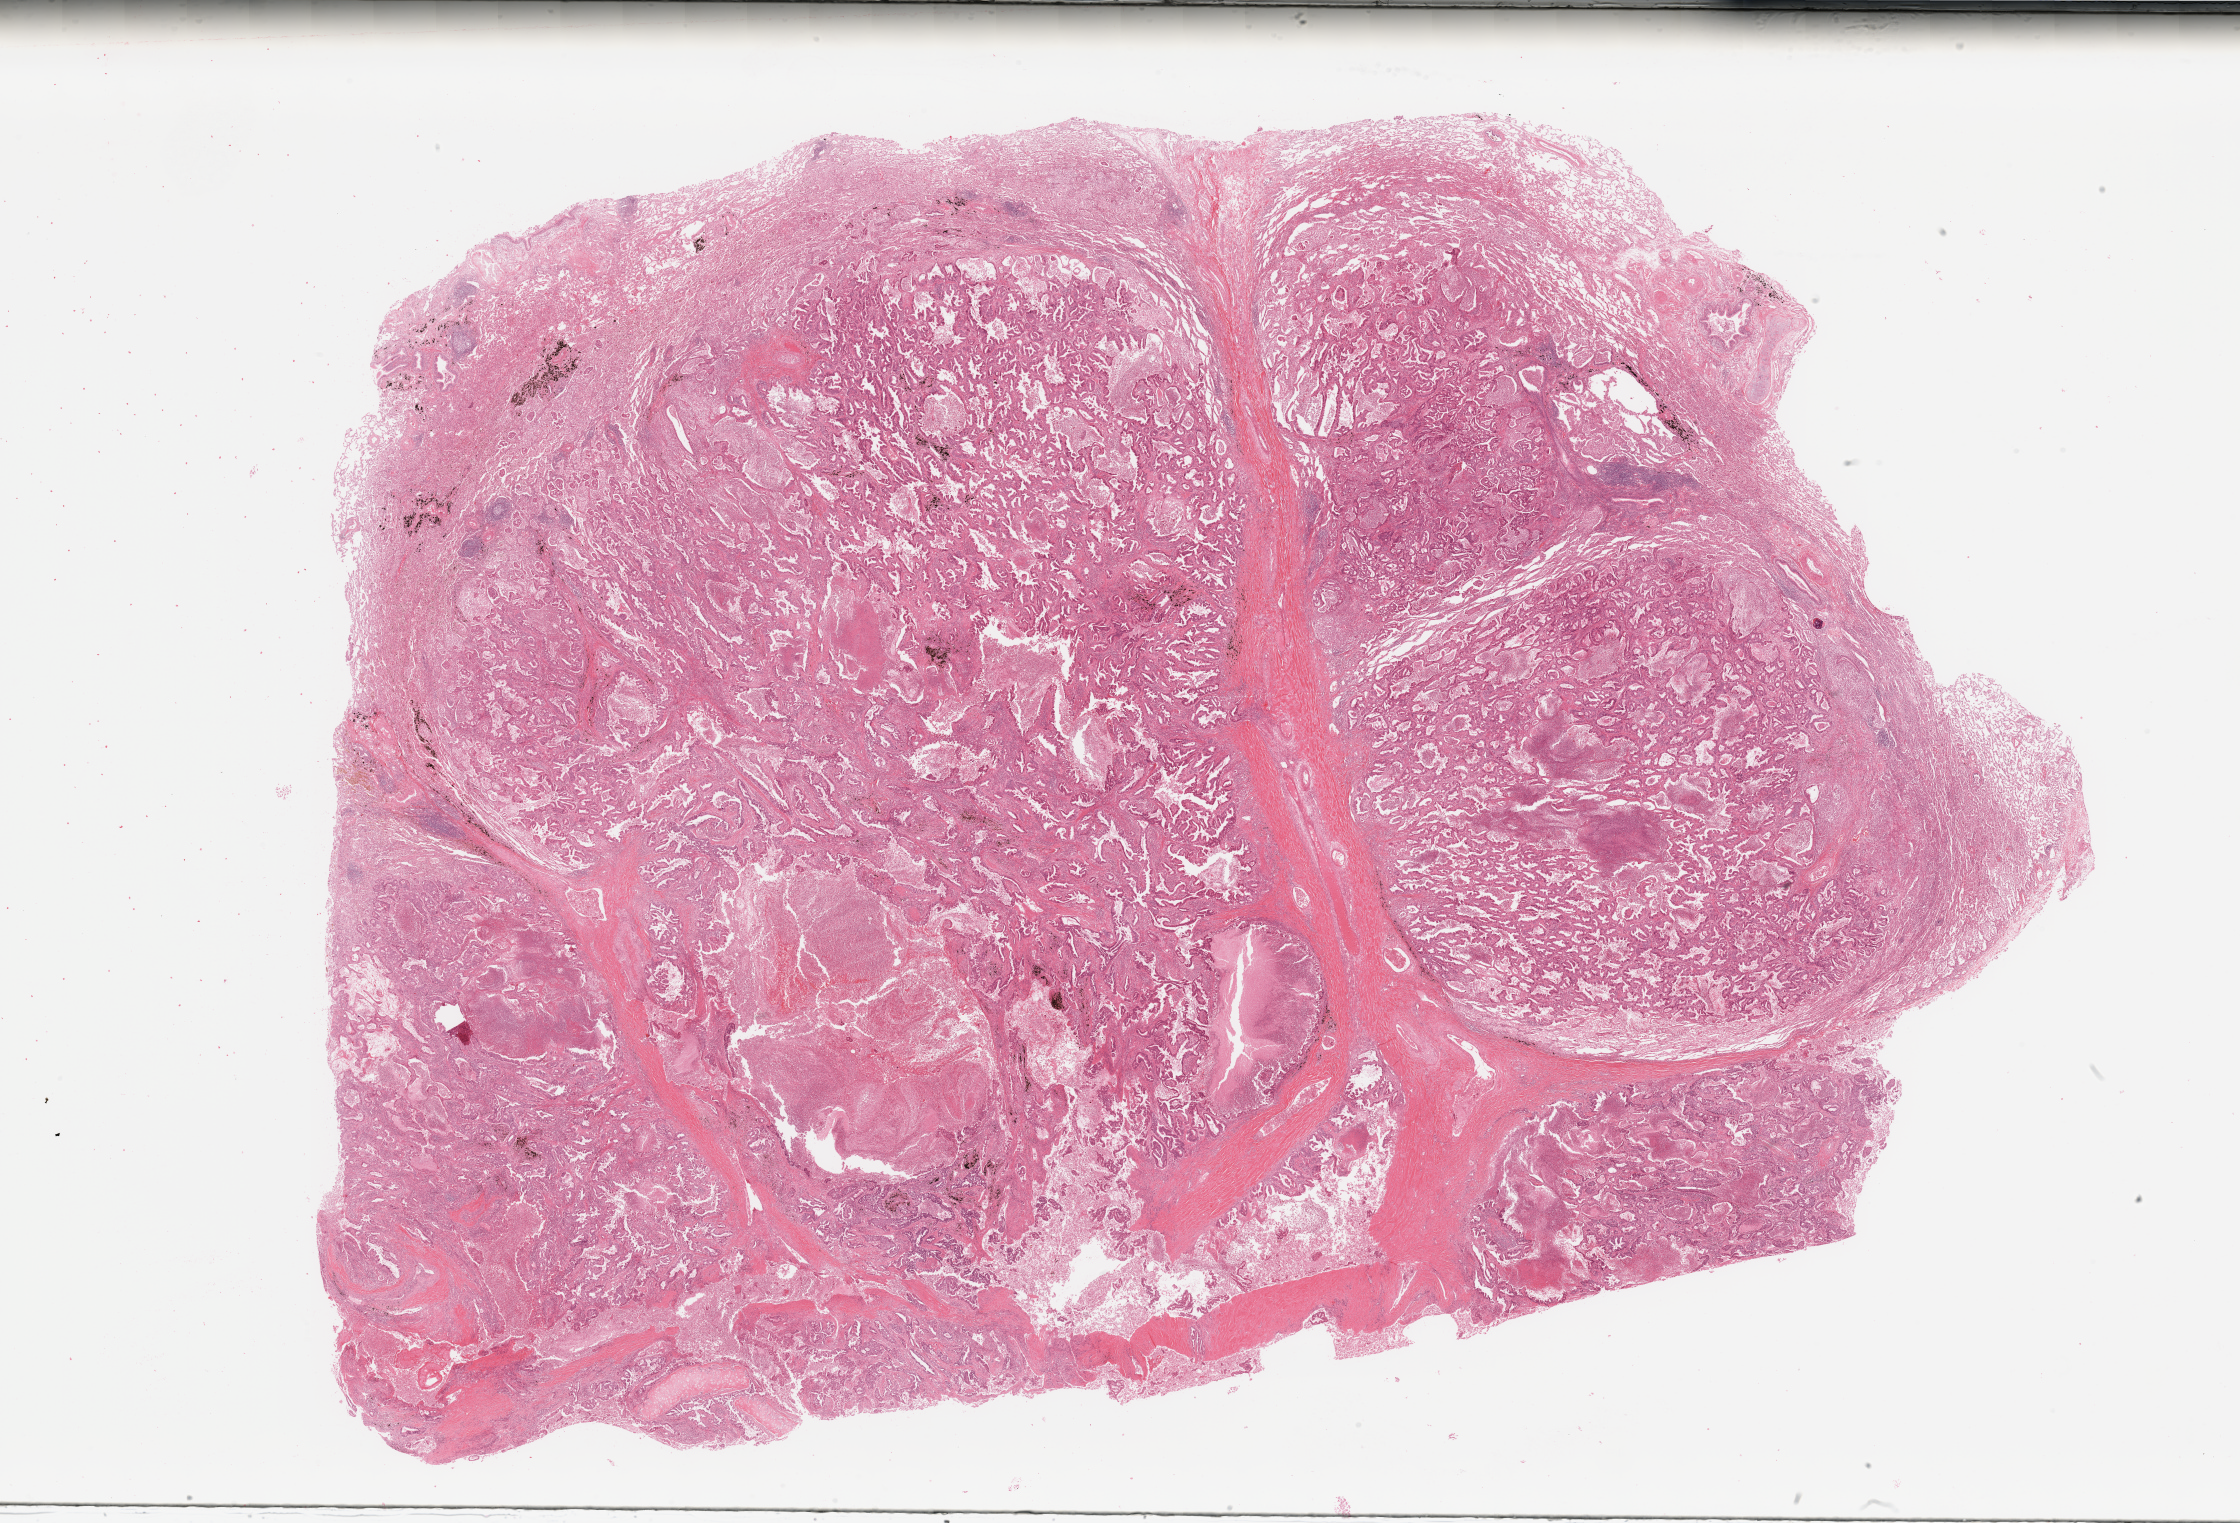
Digitized H&E-stained tissue section (whole slide), low-resolution overview of the scanned area, about 35.4 x 24.1 mm (slide scanned at 20x). Tumour tissue sample, lung. Patient: male, age 49 years. Histologic grade: G2 (moderately differentiated).
- histologic diagnosis: Adenocarcinoma, NOS
- AJCC pathologic stage: IIB